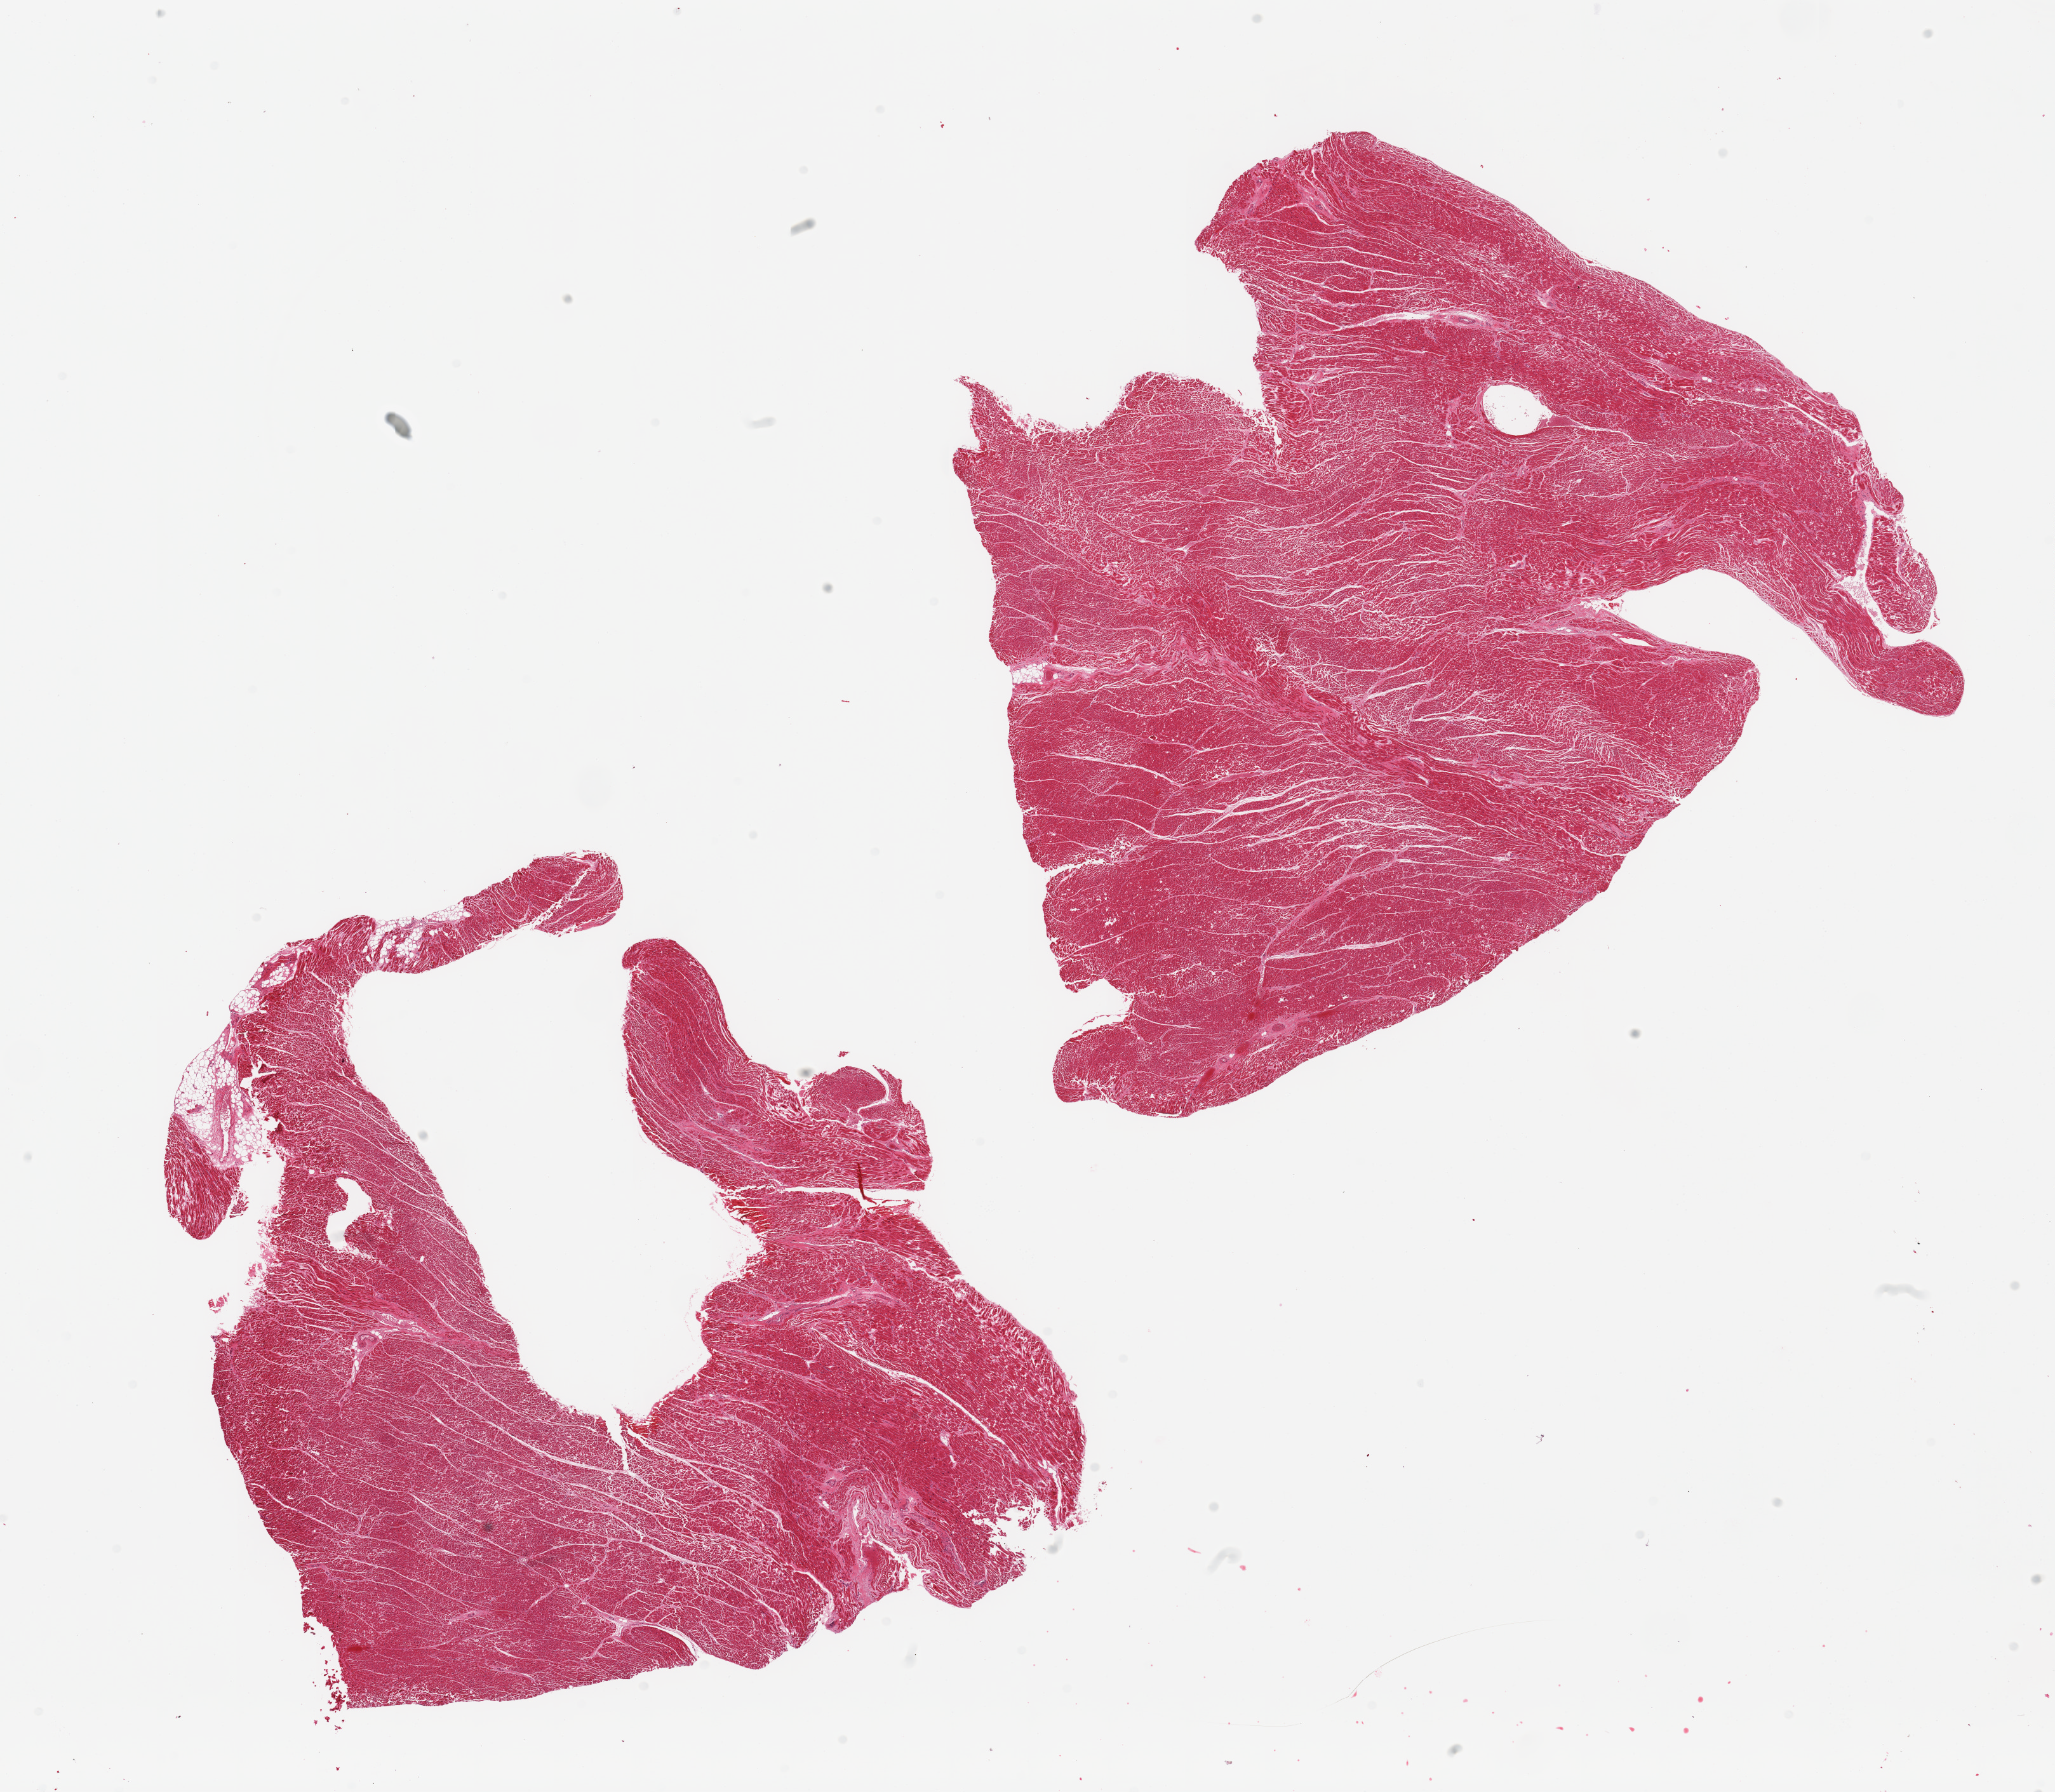
Haematoxylin and eosin whole-slide image — shown as a low-resolution overview of the whole scanned area (about 25.6 x 22.3 mm, from a 20x scan); PAXgene-fixed paraffin-embedded (PFPE) section; target tissue: heart; tissue donor sample. Male donor.
- review note (as recorded): 2 pieces; patchy hypereosinophilia (possible early ischemia)